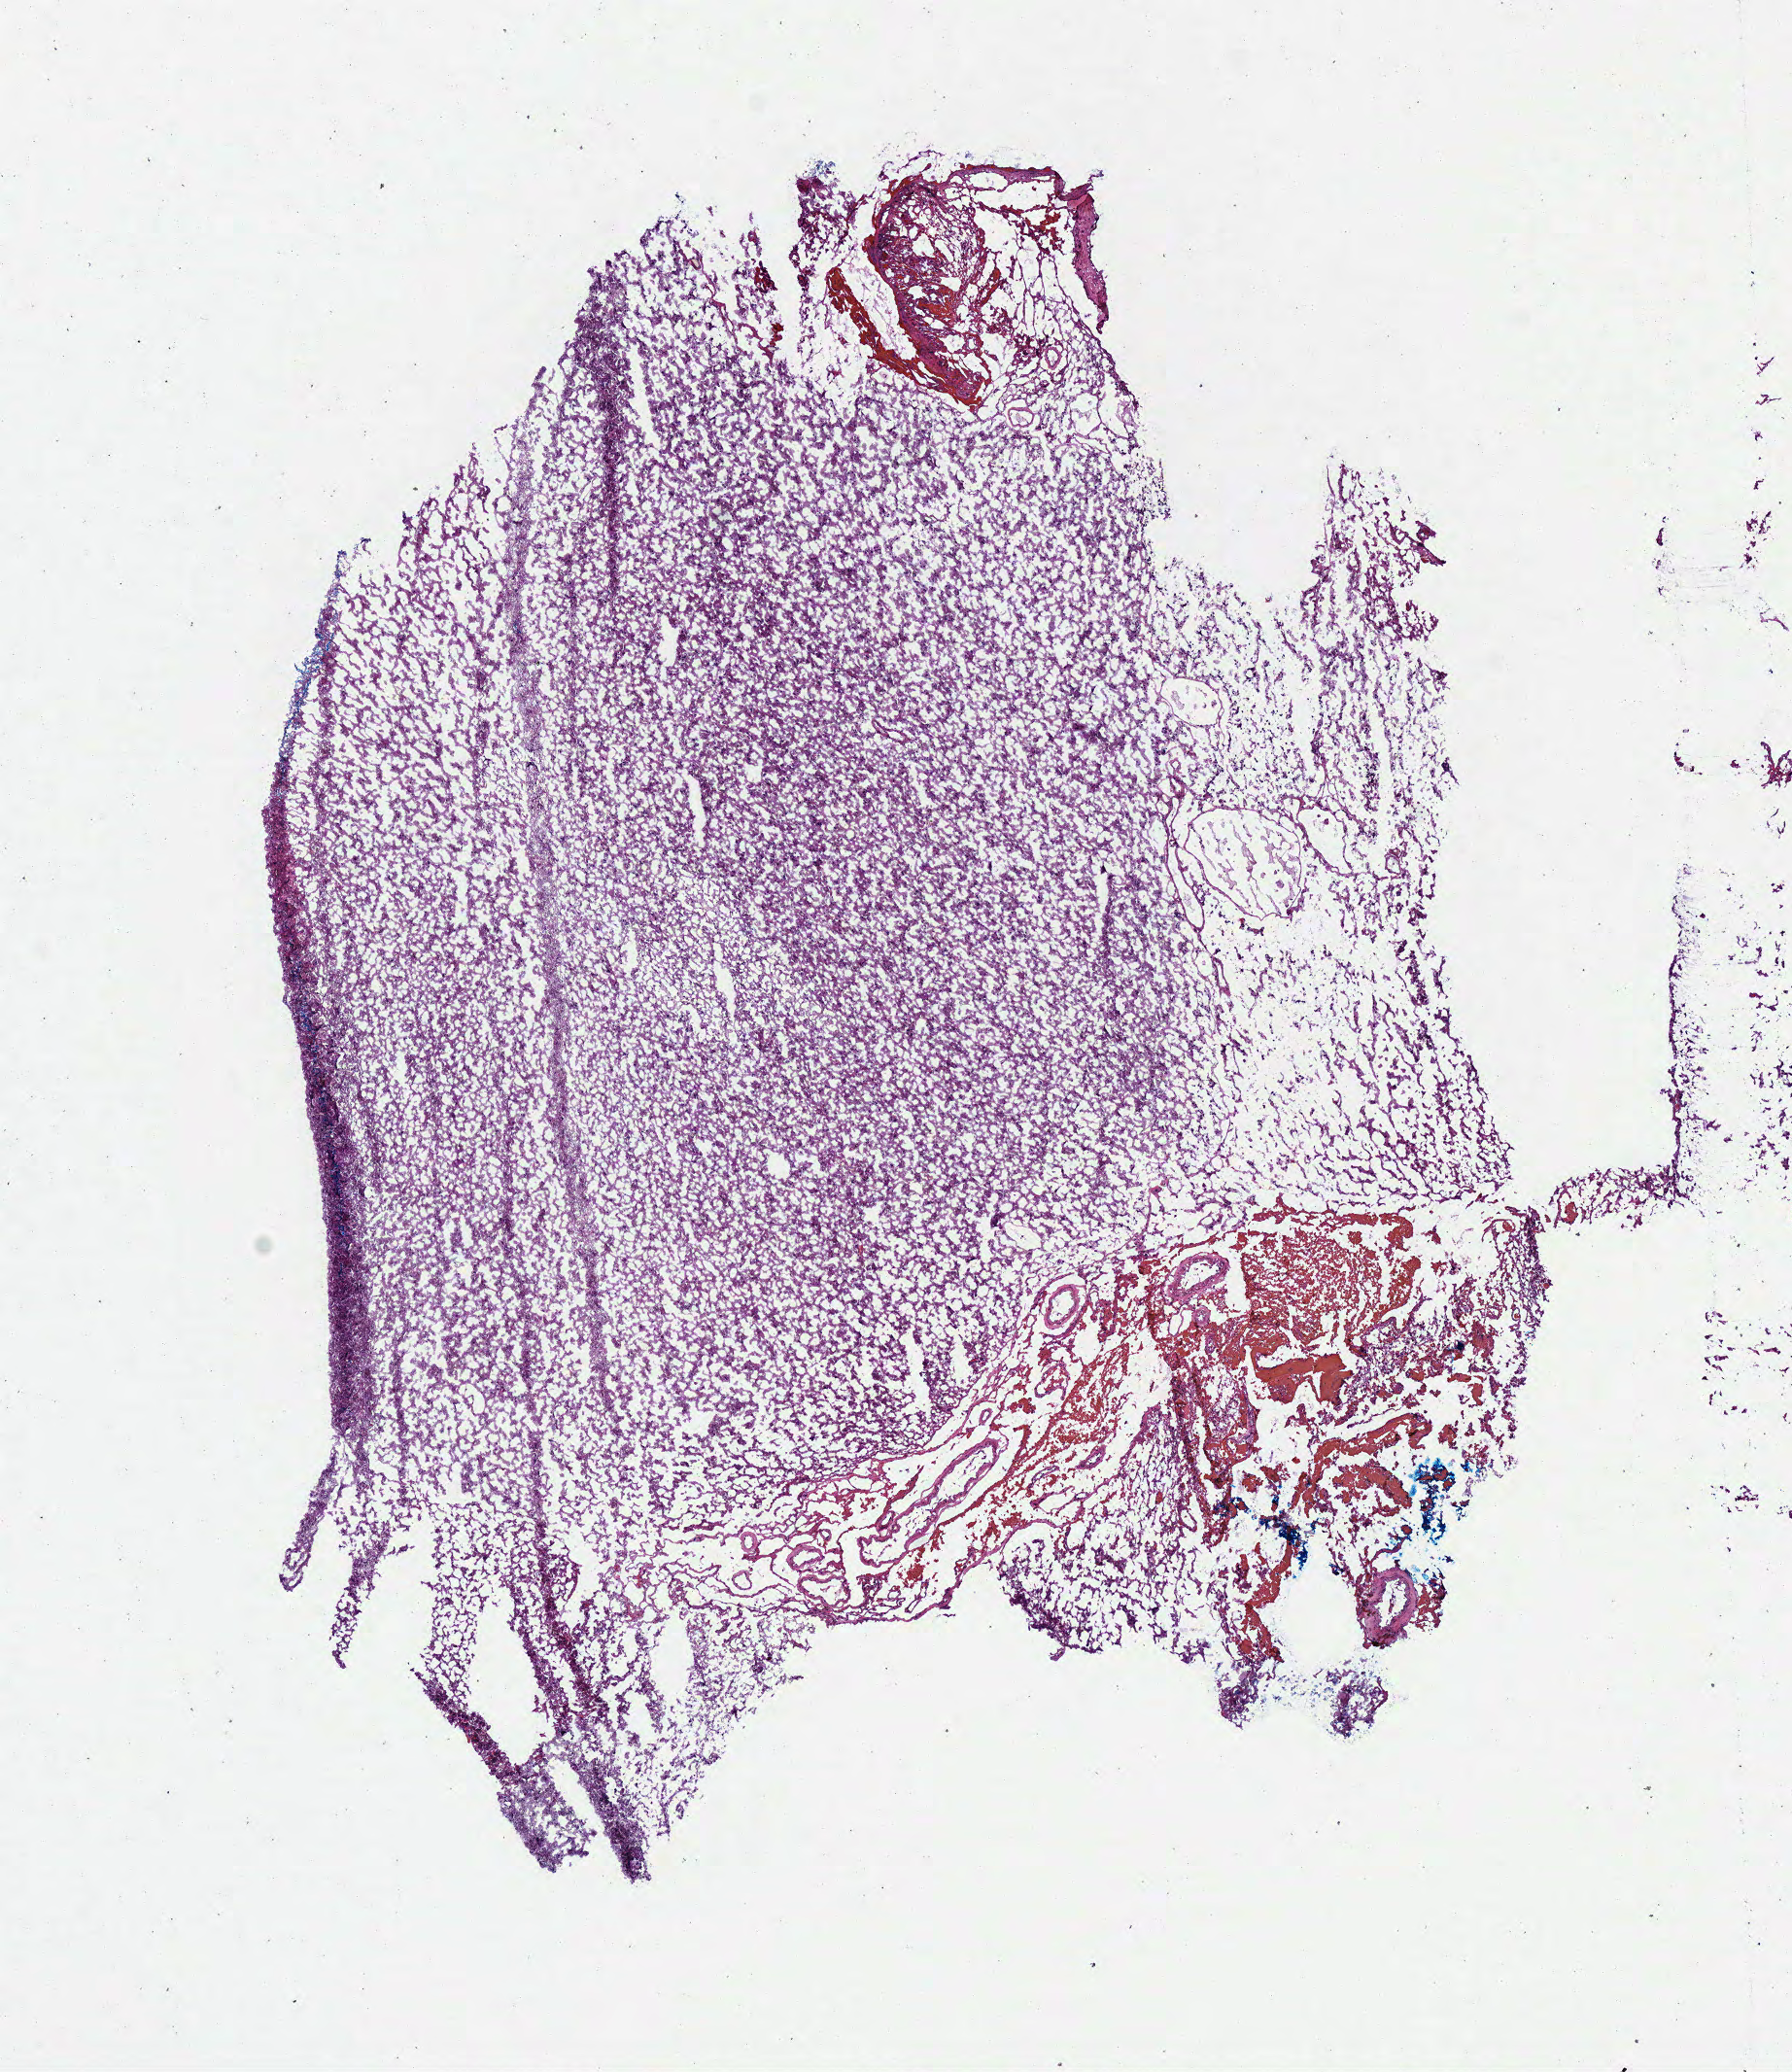
Whole-slide histology image, Hematoxylin and eosin (H&E) stained — low-resolution overview of the scanned area, about 7.3 x 8.4 mm. Frozen section. Brain, primary tumour sample. Male, age 62 years at initial diagnosis. Histologic grade: G2 (moderately differentiated). Composition of this section per pathologist review: tumour cells 90%, tumour nuclei 70%, normal cells 0%, stromal cells 10%, necrosis 0%.
Laterality: left. Diagnosis: Oligodendroglioma, NOS (cerebrum).